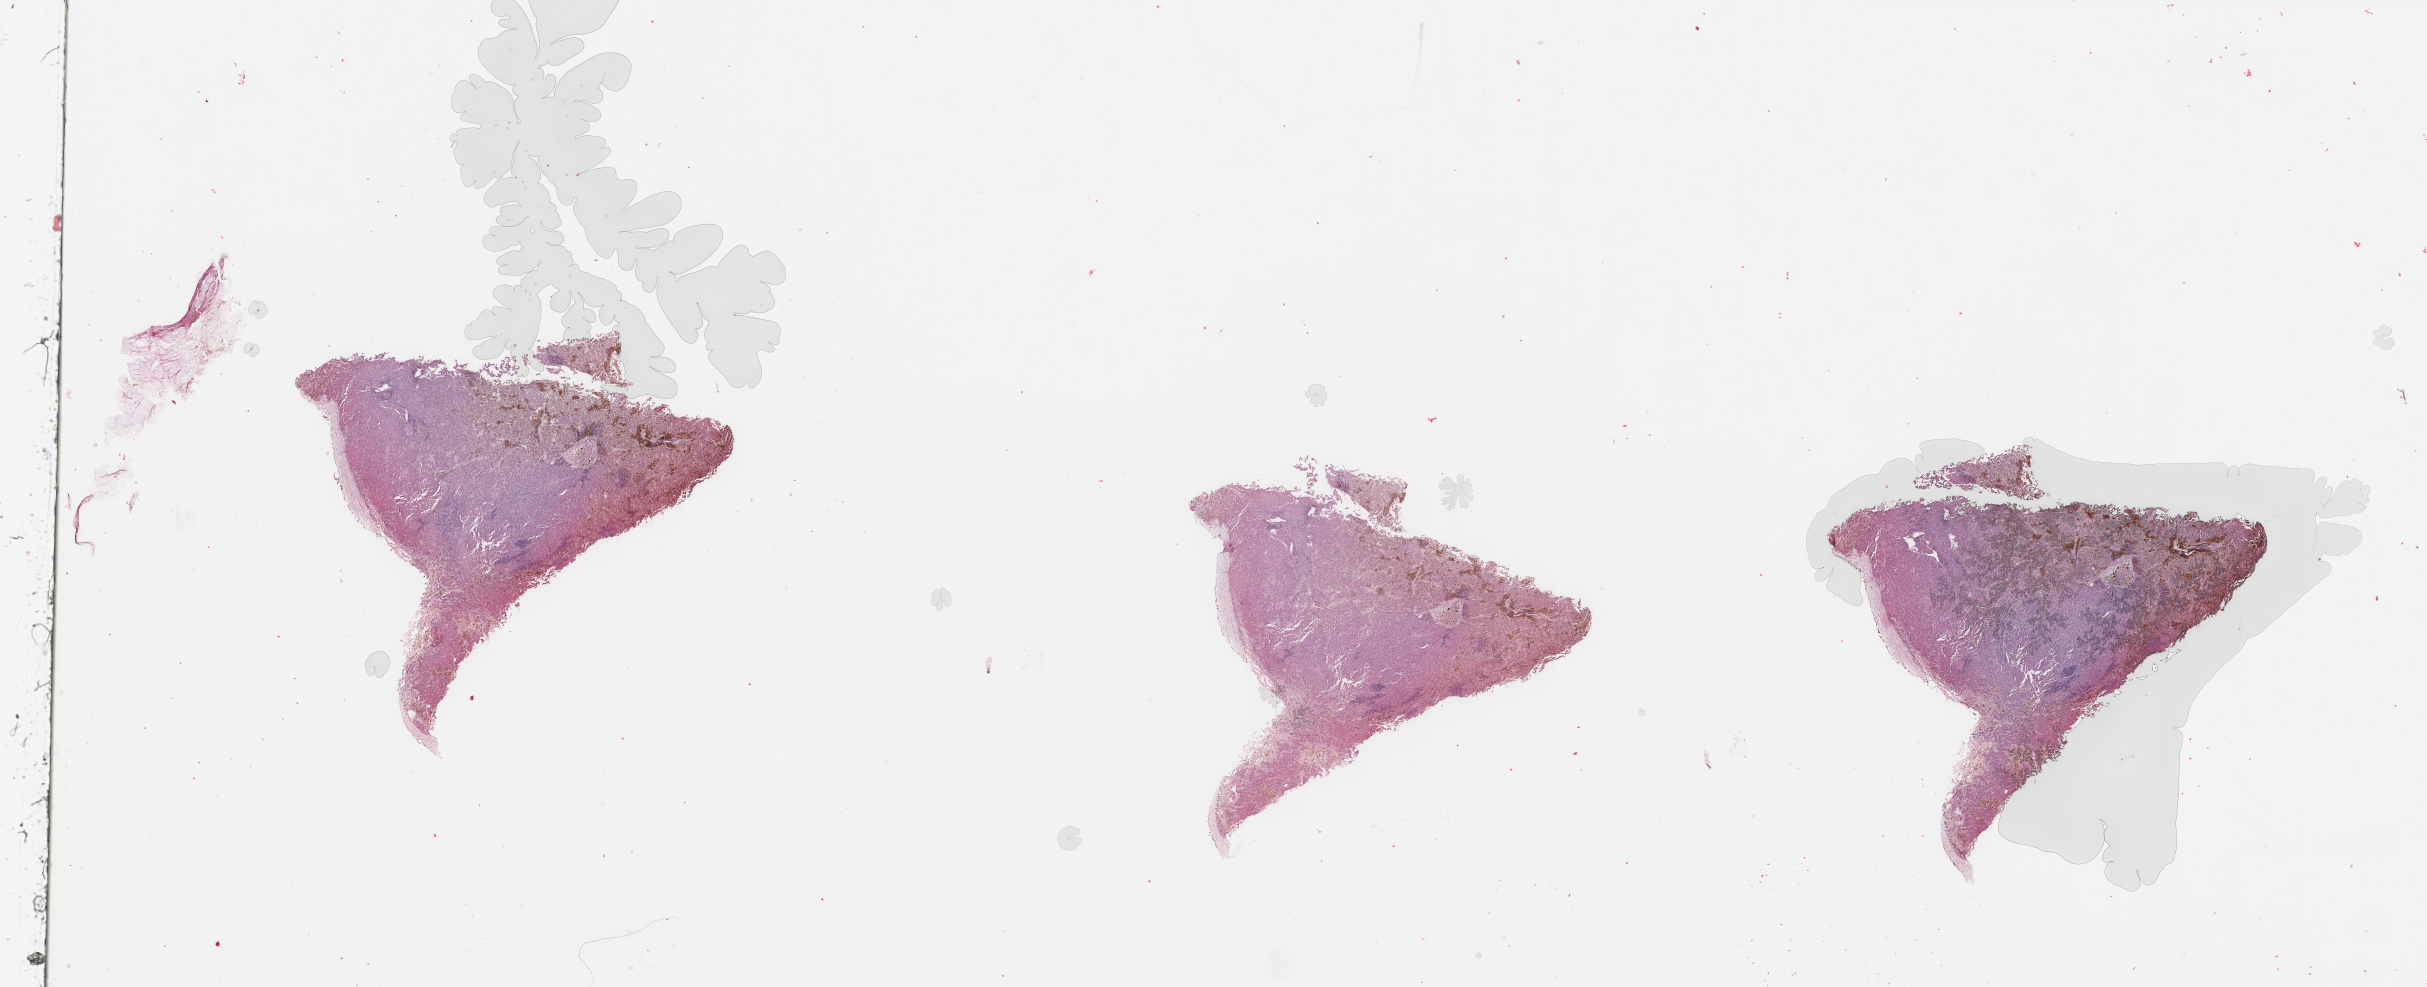
Digitized H&E-stained tissue section (whole slide), low-resolution overview of the scanned area, about 38.4 x 15.6 mm (from a 20x scan), tumour tissue sample, sampled site: lymph node. Male, 75 y/o. Slide review estimates, as recorded: tumour nuclei 90%, necrosis 0%.
This section: metastatic tumour tissue. Patient diagnosis: Malignant melanoma, NOS.